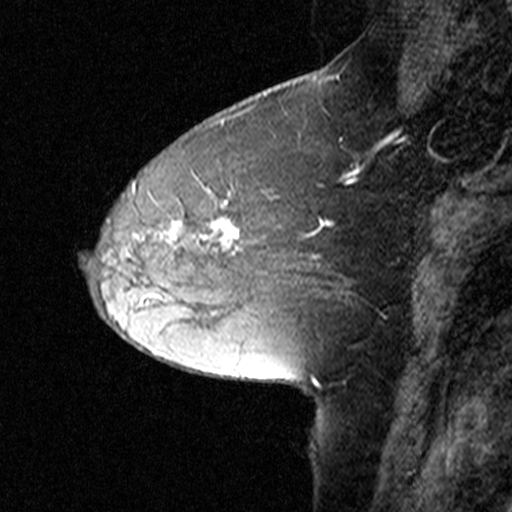
Breast MRI (dynamic contrast-enhanced), one sagittal slice; slice 17 of 44 in the series (ordered by position); dynamic contrast-enhanced study with each time point stored as its own series, time point 2 of 3 at this slice position (early post-contrast, ordered by acquisition time); 1.5 T; TE 4.5 ms, TR 11 ms; 3 mm slice thickness; 512 × 512 image matrix. Patient: female, 50 years. From the clinical record (not read from this slice): setting: breast cancer imaged before/during neoadjuvant chemotherapy; receptor status: HR-positive, HER2-negative.
Annotated regions visible in this slice (semi-automatically segmented with operator editing):
- analysis volume of interest (the breast-tissue region the enhancement analysis was run in; not a lesion): bounding box [x1, y1, x2, y2] px = [126, 162, 312, 291]
- tumour enhancement mask (voxels above the 90 % enhancement threshold inside the analysis volume of interest): [133, 181, 238, 248]